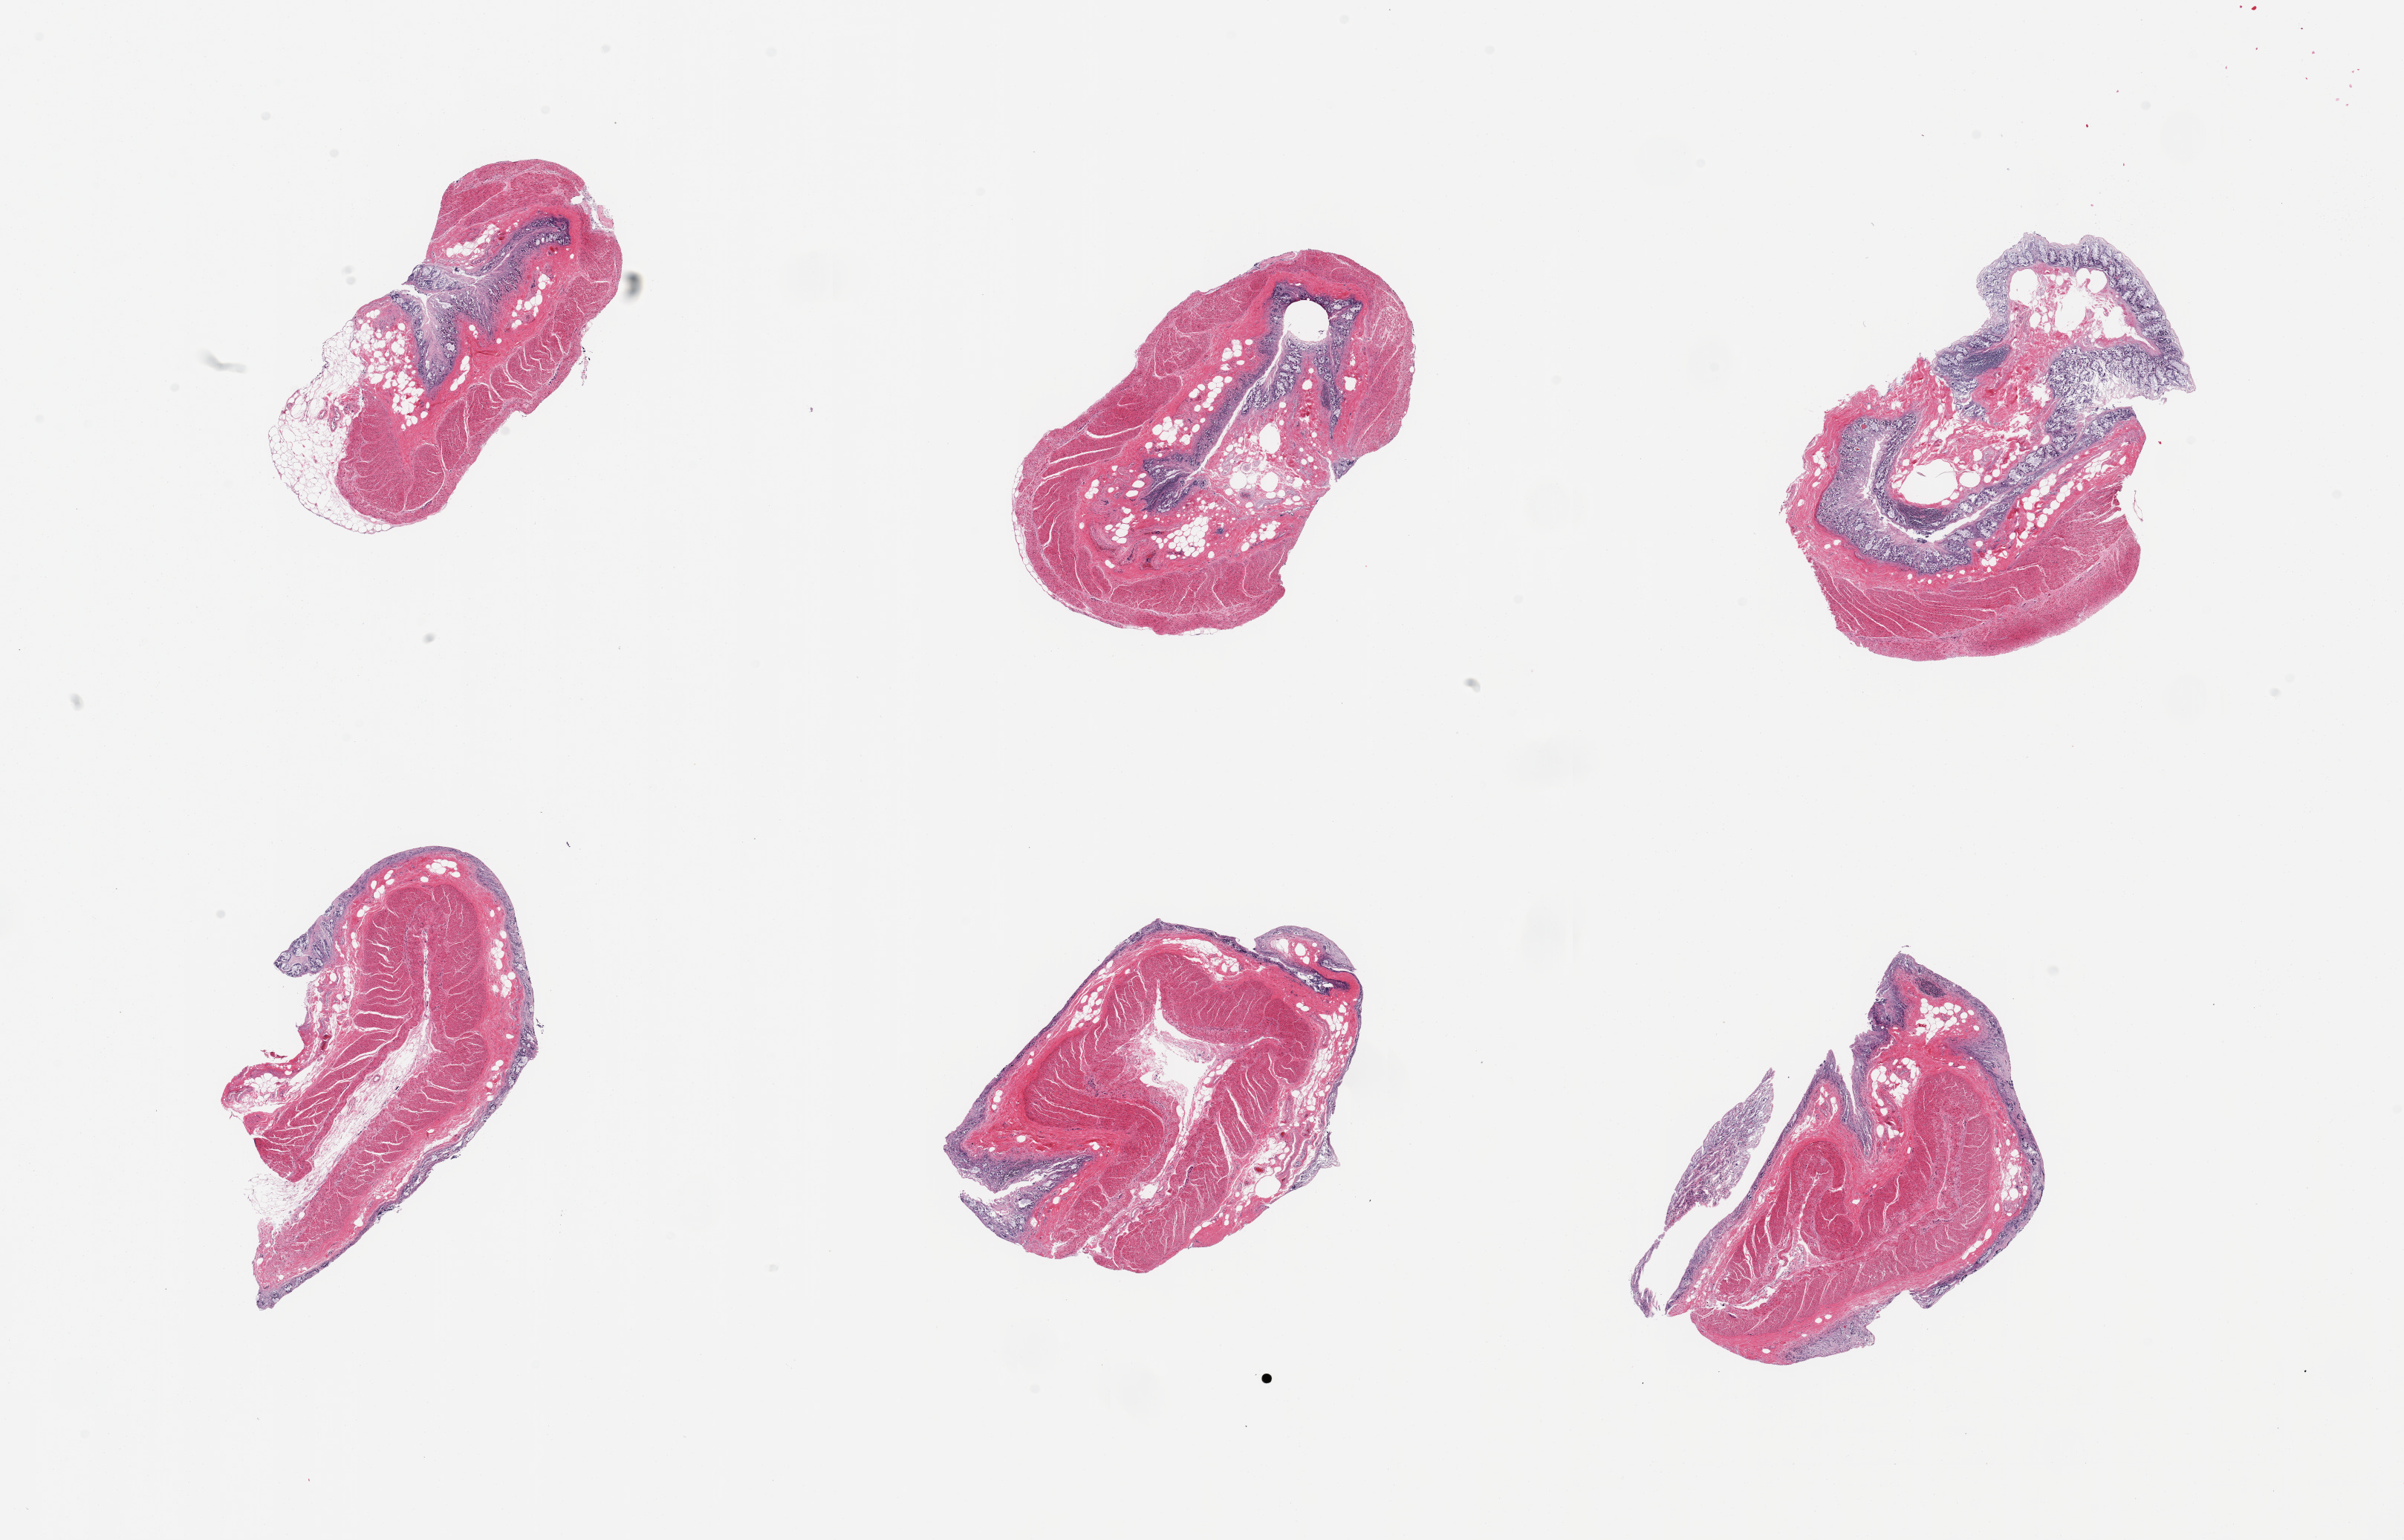
Haematoxylin and eosin whole-slide image, a low-resolution overview of the entire scanned area, about 25.6 x 16.4 mm. PAXgene-fixed, paraffin-embedded tissue. Target tissue: transverse colon. Donor tissue sample. Male donor.
Review note (as recorded): 6 pieces, target mucosa with sloughed mucosal ductal elements, residual lamina propria is ~0.1mm.